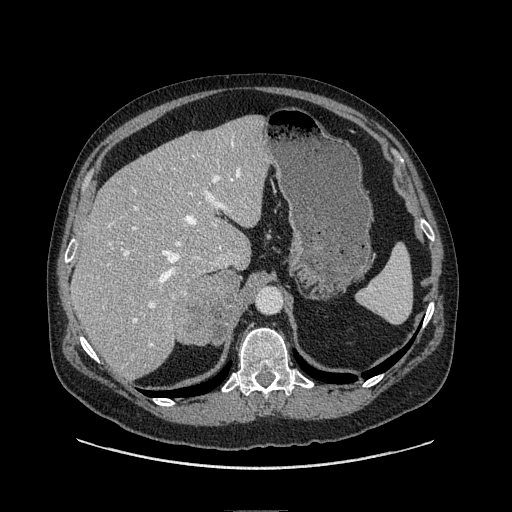
Contrast-enhanced abdominal CT, one axial slice; soft-tissue window (W 400 / L 40 HU); 512 × 512 image matrix. Male patient. From the clinical record (not read from this slice): diagnosis: adrenocortical carcinoma; tumour side: right adrenal; tumour size at pathology: 7.5 cm; Ki-67 index: 15 %.
Outlined on this slice (semi-automatic segmentation, software-assisted and operator-edited):
- mass: box from (x=175, y=268) to (x=240, y=346) px